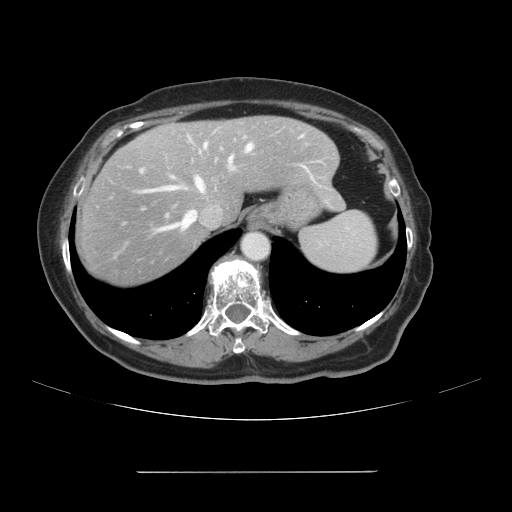
Contrast-enhanced abdominal CT, one axial slice; position 84 of 111 along the scan axis; 120 kVp; intravenous contrast given; soft-tissue window (W 400 / L 40 HU); 512 × 512 image matrix, field of view 400 × 400 mm. Female patient, age 74 years. From the clinical record (not read from this slice): diagnosis: colorectal cancer liver metastases, imaged before liver resection.
Annotated regions visible in this slice (expert manual segmentation):
- hepatic veins: bounding box <144,145,252,228> (left, top, right, bottom; pixels)
- liver: <75,117,343,289>
- planned liver remnant (the part of the liver to remain after resection): <164,117,344,219>
- portal vein (with intrahepatic branches): <141,151,234,172>